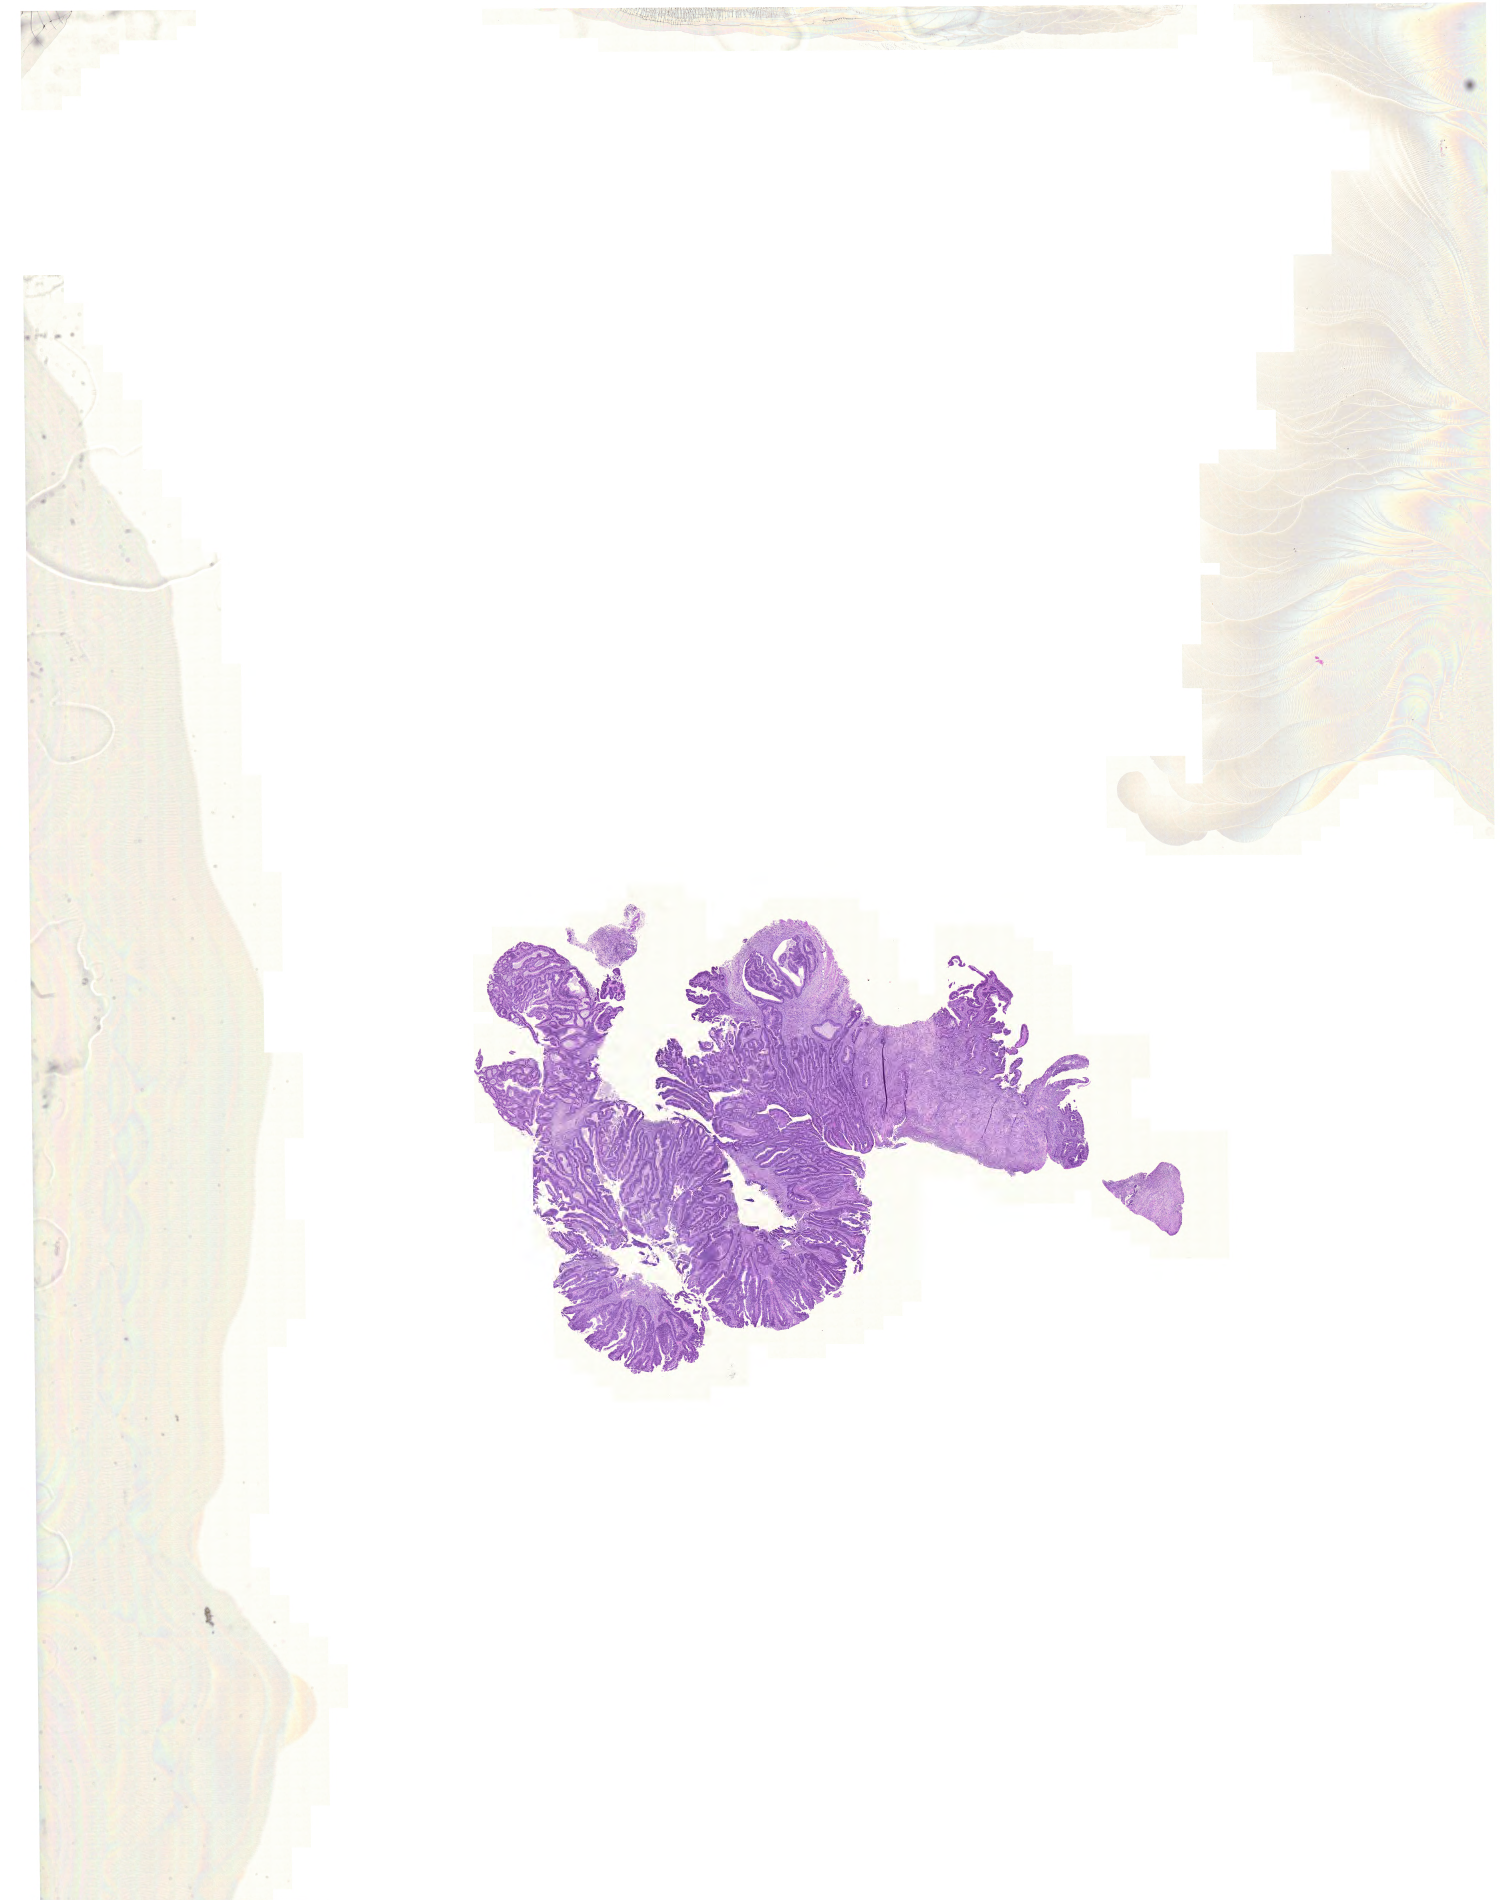
Digitized Hematoxylin and eosin (H&E) stained tissue section (whole slide), whole scanned area (about 22.3 x 28.3 mm, acquisition: 20x scan) shown as a low-resolution overview. Formalin-fixed paraffin-embedded (FFPE) diagnostic section. Sample: primary tumour, colon. Patient: female, age at initial diagnosis 78 years.
Diagnosis: Adenocarcinoma, NOS.